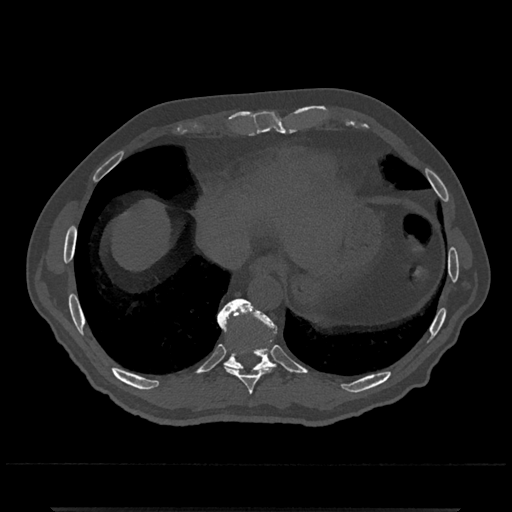
CT including the spine, one axial slice; position 587 of 797 along the scan axis; reconstruction kernel Br40s/3; 120 kVp; bone window (W 1800 / L 400 HU); 0.5 mm slice thickness; 512 × 512 image matrix, field of view 393 × 393 mm. Male patient, age 67 years. From the clinical record (not read from this slice): primary cancer: prostate.
Annotated regions visible in this slice (semi-automatically segmented with operator editing):
- T10 vertebra: bounding box (x1, y1, x2, y2) in pixels: (218, 299, 276, 373)
- T9 vertebra: (219, 320, 269, 395)